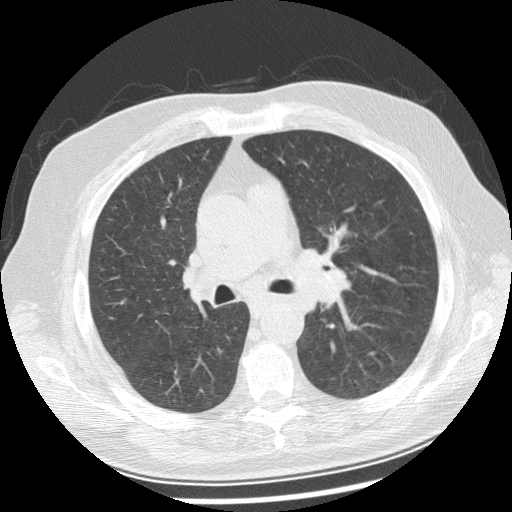
Low-dose screening chest CT, one axial slice. 120 kVp. Lung window (W 1500 / L -600 HU). 2.5 mm slice thickness. 512 × 512 image matrix.
Outlined on this slice (manually delineated by an expert):
- lesion 1 (tumor, left main bronchus): box from (x=312, y=267) to (x=352, y=307) px